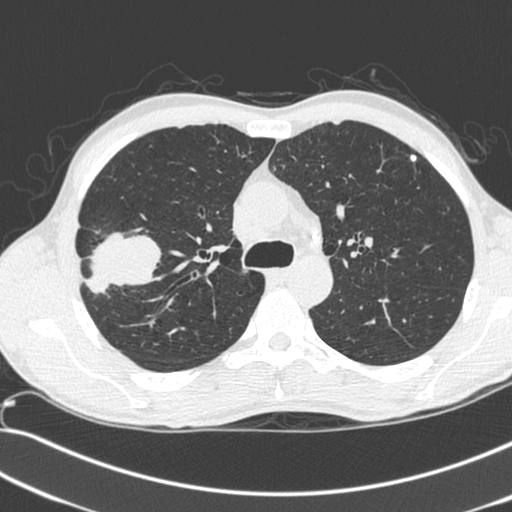
Low-dose screening chest CT, axial slice. First (baseline) screen. Lung window (W 1500 / L -600 HU). 1.3 mm slice thickness. 120 kVp. Slice 78 of 281 in the series. 512 × 512 image matrix. Male participant, aged 55 years at enrolment.
• Expert reader's lesion annotation, bounding box [x1, y1, x2, y2] px = [71, 231, 153, 304].
• Screening reader's record for this exam (one nodule recorded; not confirmed to be the boxed lesion): non-calcified nodule or mass ≥4 mm, right upper lobe, 52 × 39 mm, spiculated (stellate) margins, soft tissue attenuation.
• Lung cancer was diagnosed 25 days after this screen: large cell neuroendocrine carcinoma, right upper lobe, poorly differentiated (G3), stage IIB (AJCC 6th edition), 49 mm at pathology.